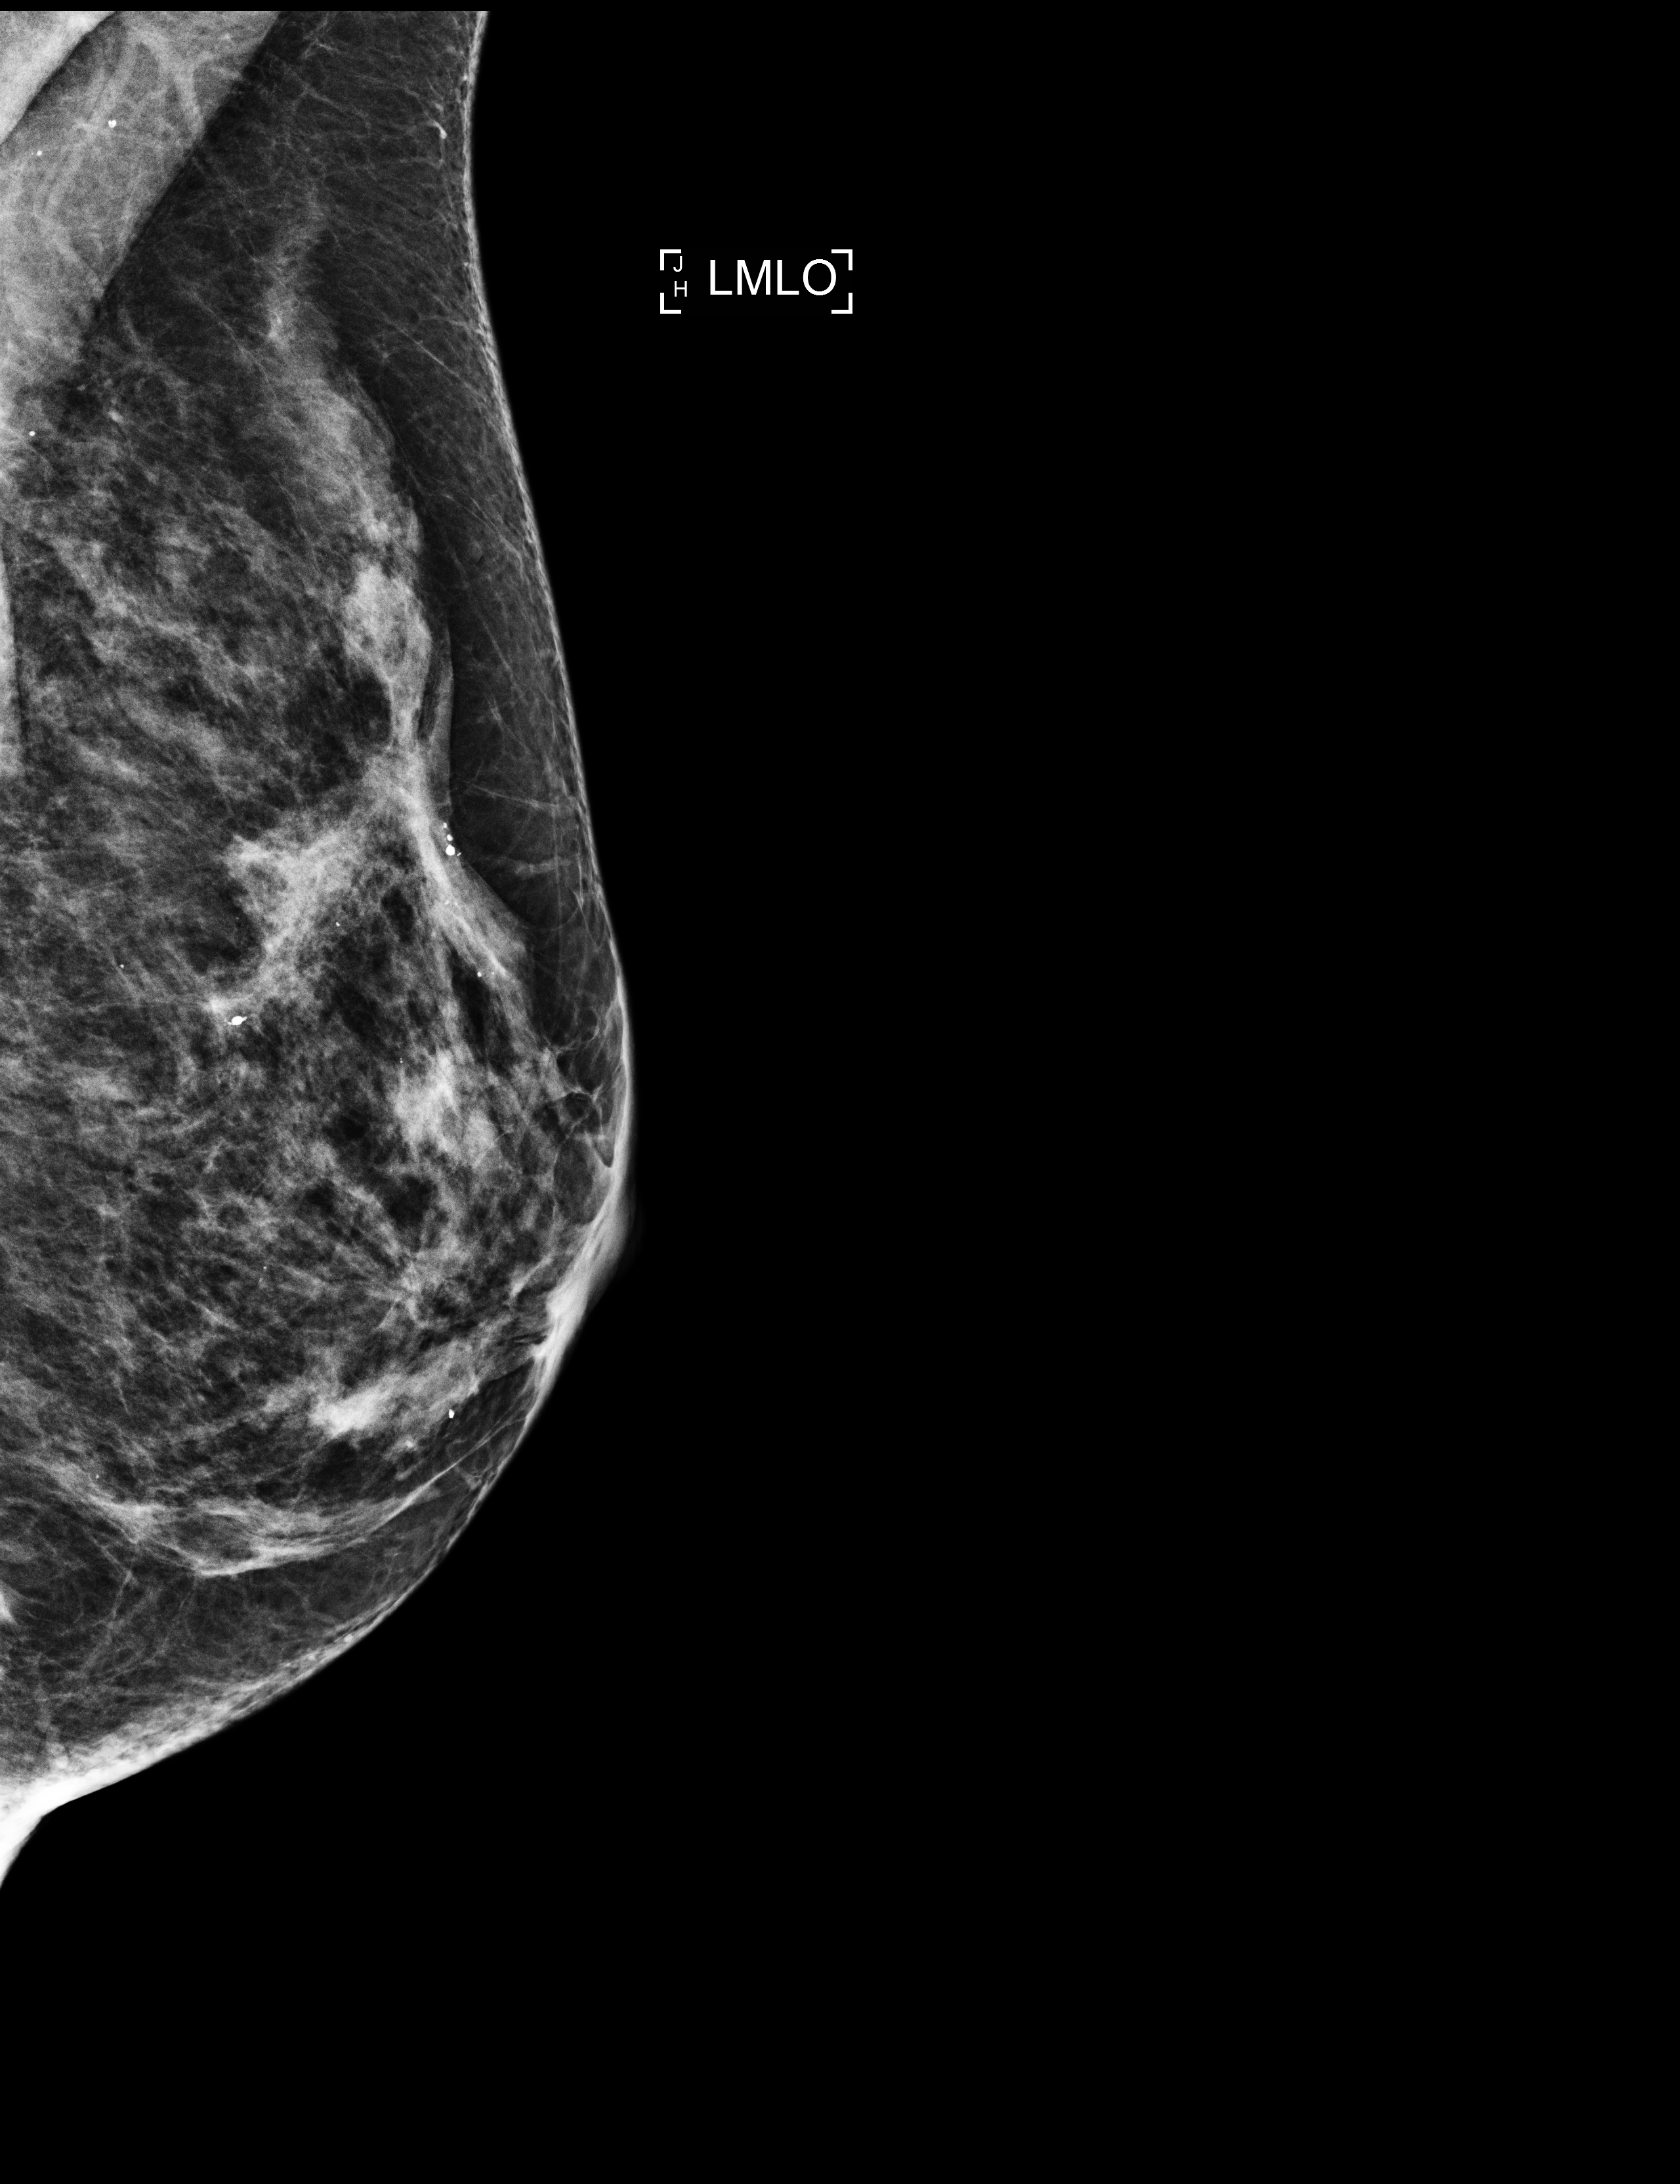
Full-field digital mammogram (FFDM); left breast; MLO view; annual screening mammography examination; compressed breast thickness 44 mm. Patient: female, 74 years.
- breast density at the screening exam (both breasts): heterogeneously dense (BI-RADS density category c)
- final BI-RADS assessment for this screening round (tomosynthesis exam, both breasts): category 2
- recall: no recall after this screen